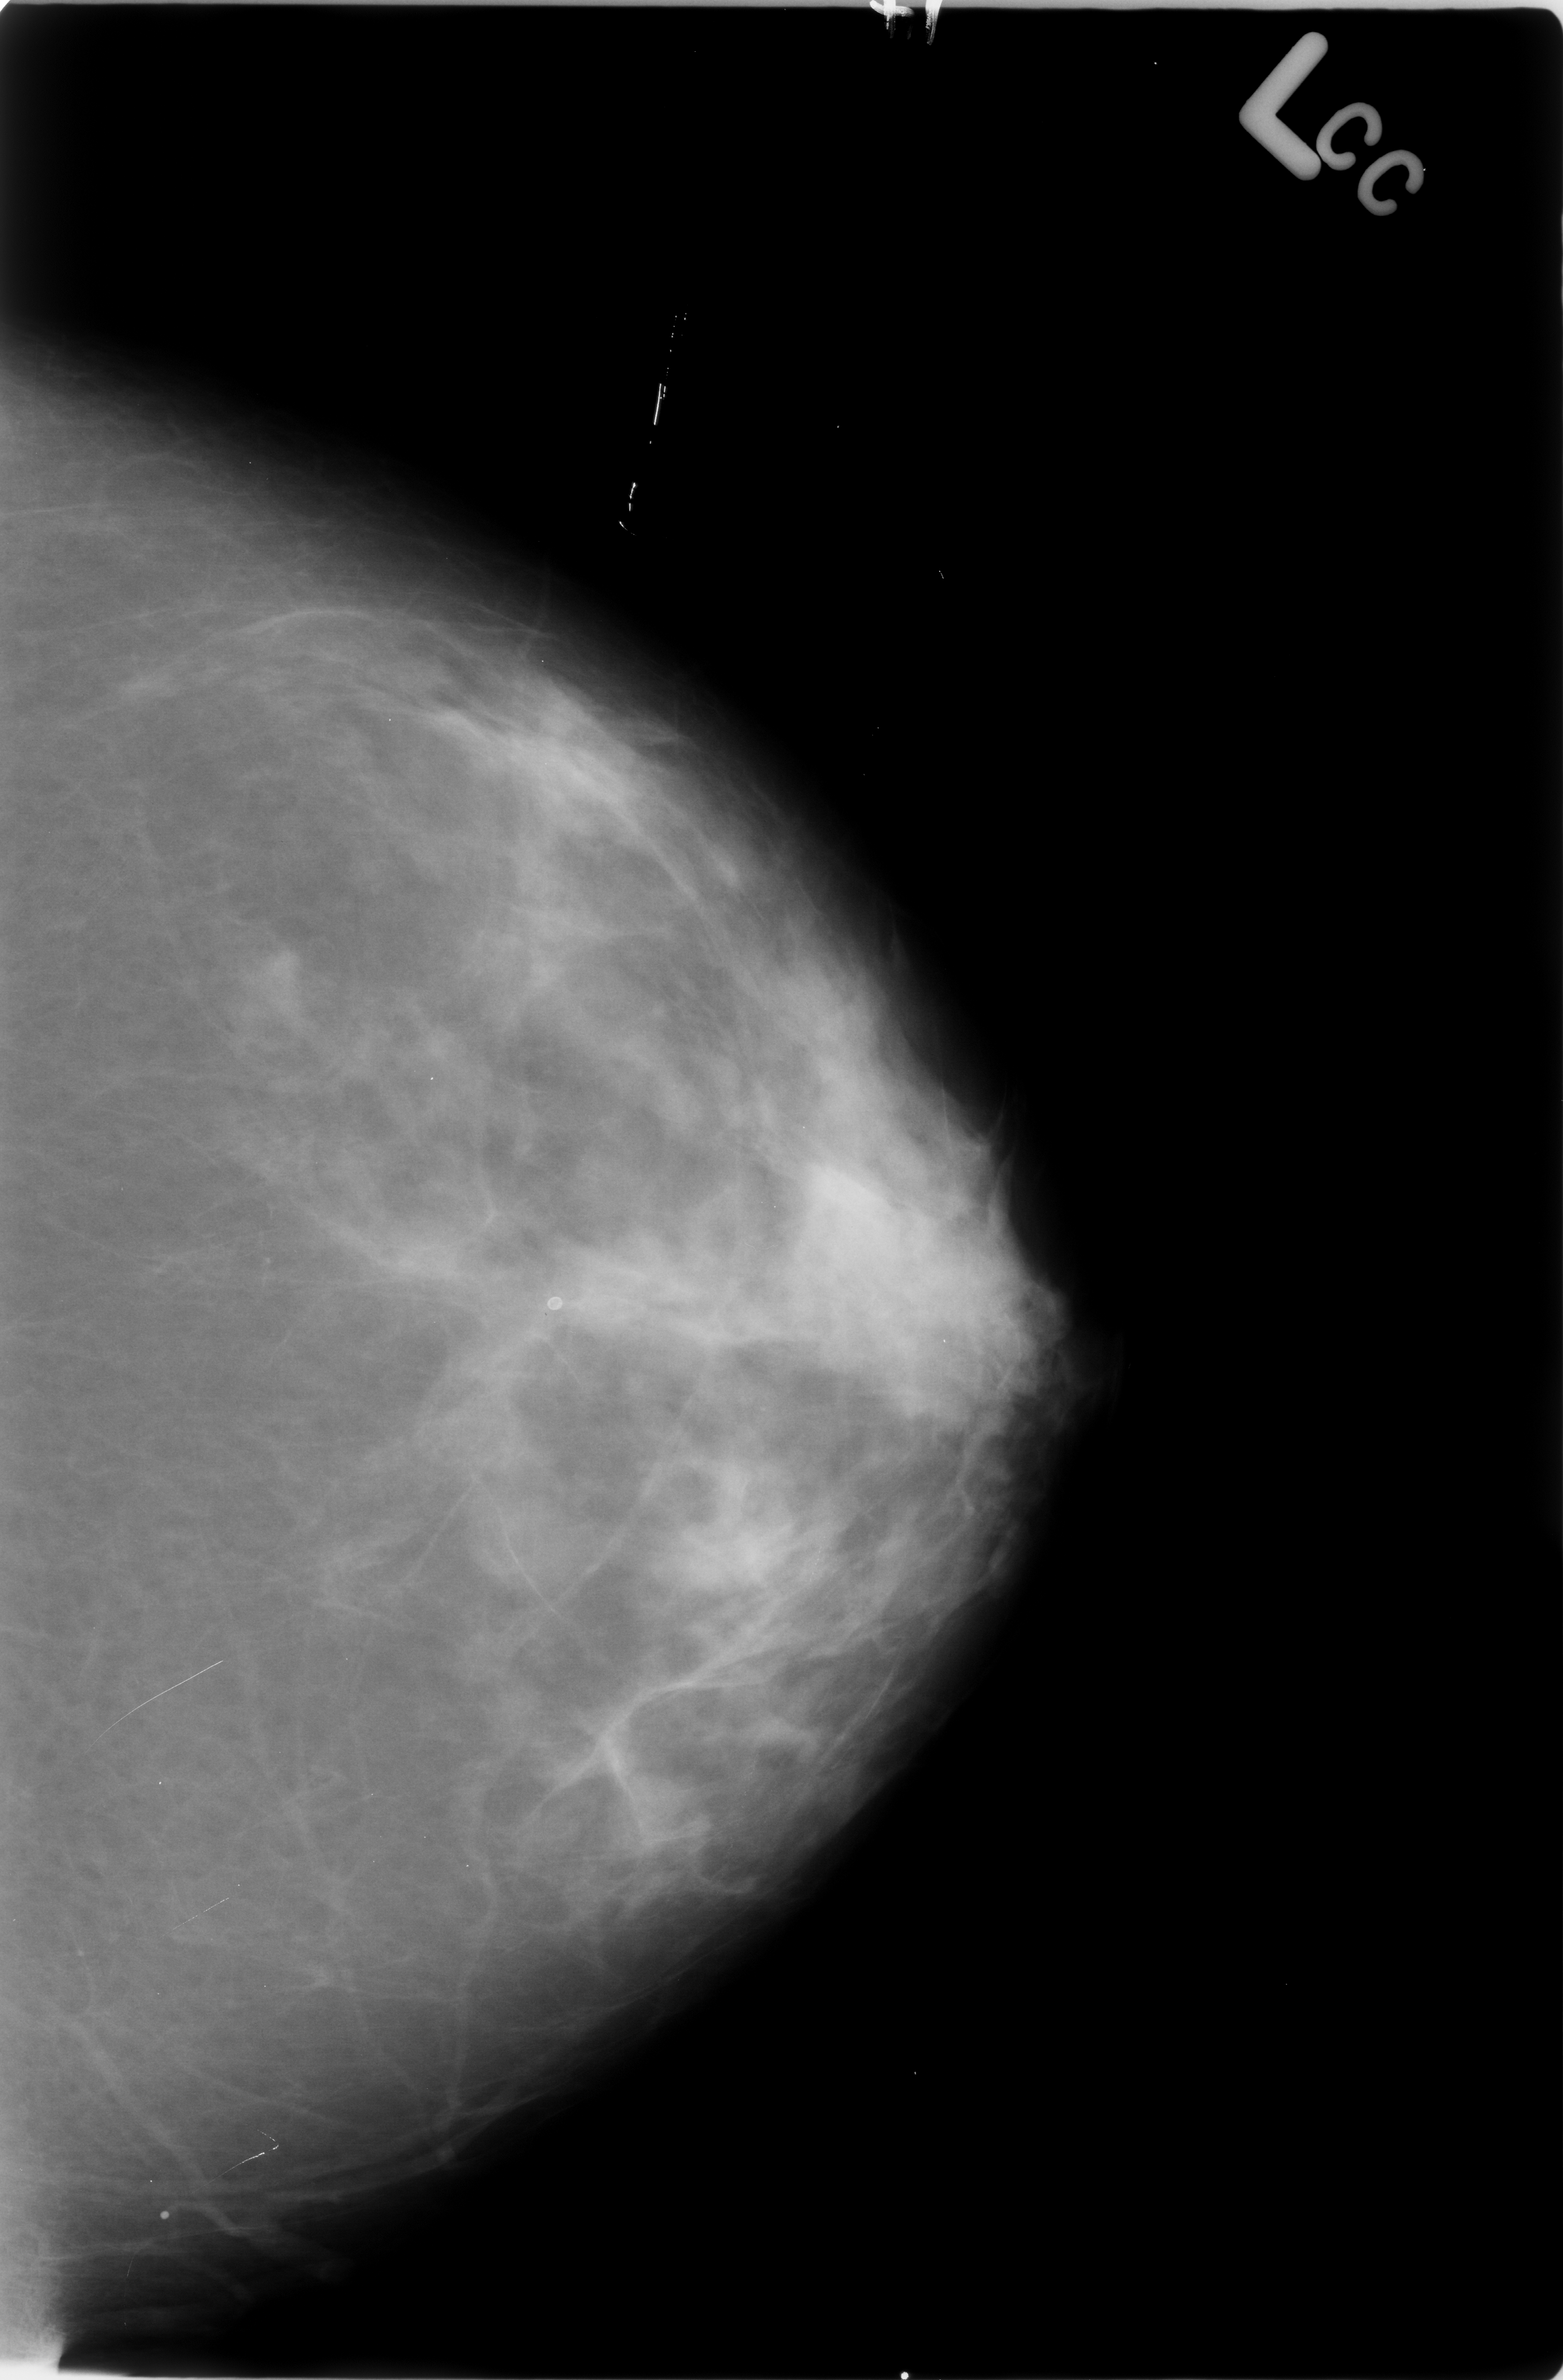
Digitized screen-film mammogram. Left breast. Craniocaudal (CC) view. 1563 × 2380 image matrix.
Expert-marked regions of interest on this film, with their recorded descriptors:
- calcifications, morphology lucent center; BI-RADS assessment category 2; outcome (as recorded, no biopsy): benign without callback (not worked up further): bounding box (x1, y1, x2, y2) in pixels: (509, 1272, 590, 1353)